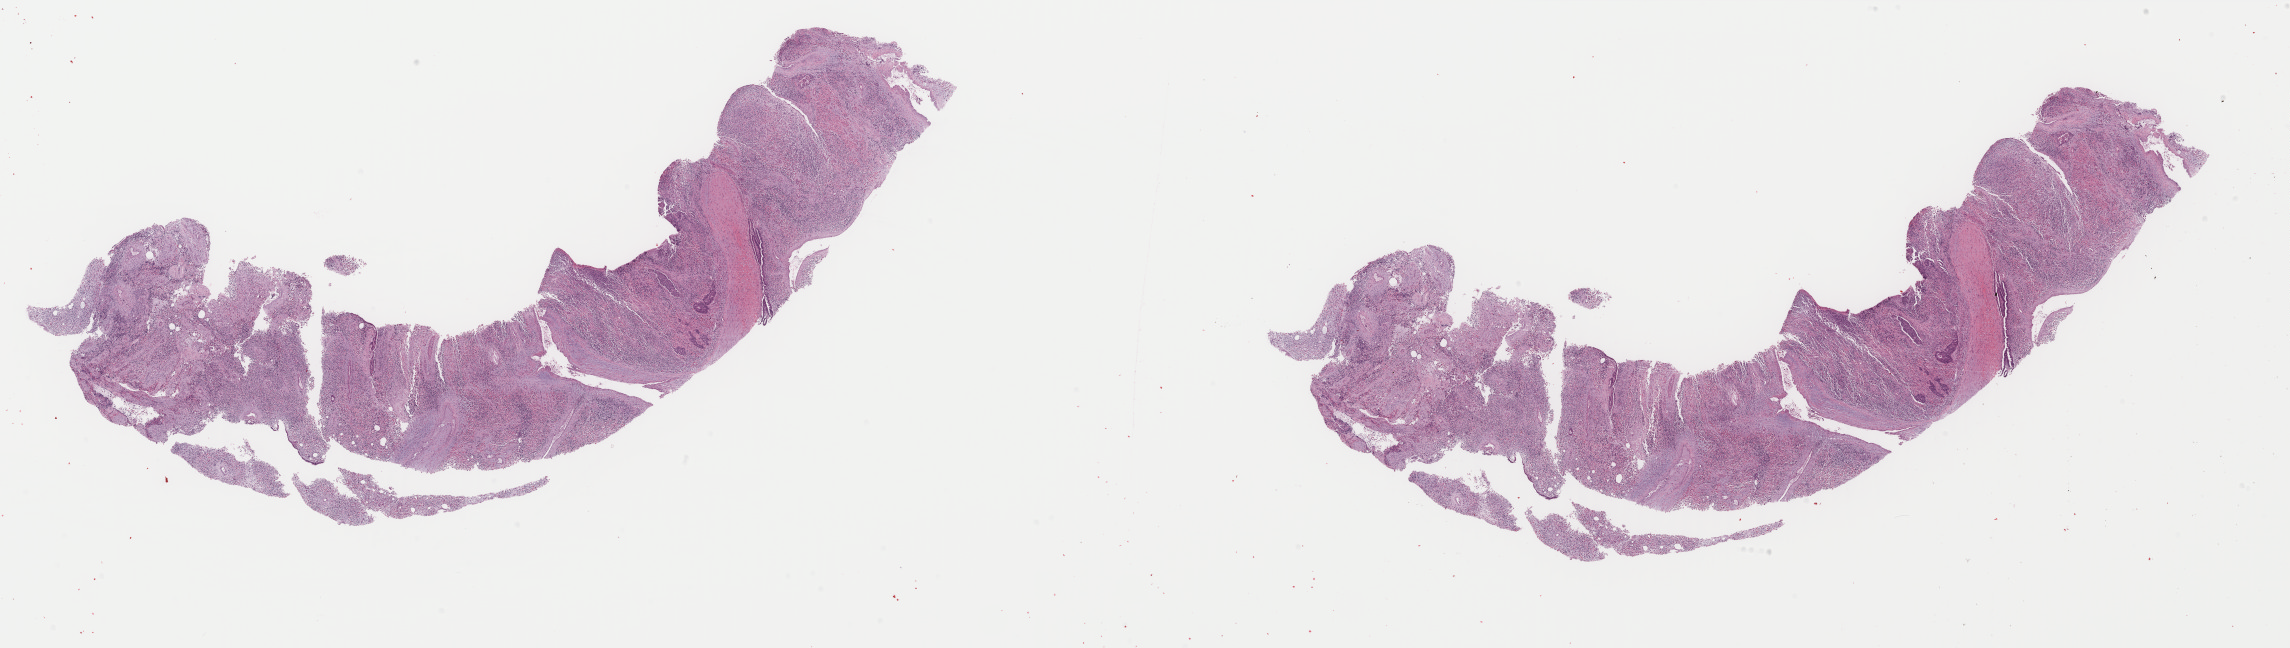
Digitized Hematoxylin and eosin (H&E) stained tissue section (whole slide) — a low-resolution overview of the entire scanned area, about 36.4 x 10.3 mm (acquisition: 40x scan). FFPE section. Sample: primary tumour, uterus. Female patient; age at initial diagnosis 61 years.
• FIGO stage: IIIC
• diagnosis: Mullerian mixed tumor
• lymph nodes positive (case pathology): 0 of 9 examined